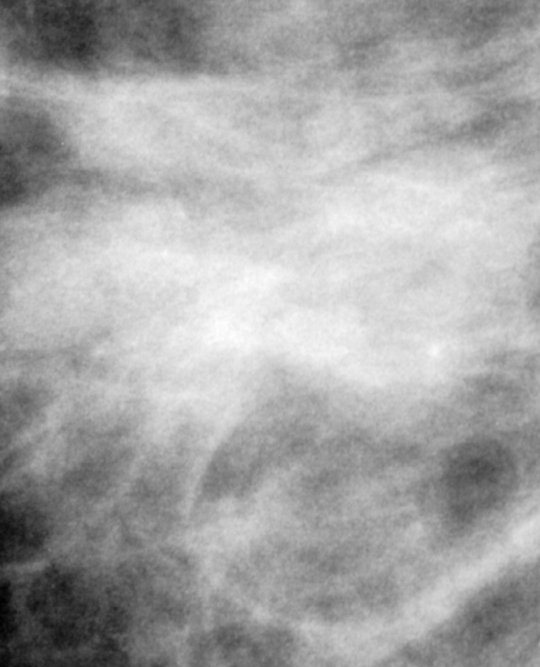
Crop from a digitized film mammogram around one marked abnormality, left breast, MLO view.
- Mass, shape irregular, margins ill defined; BI-RADS assessment category 5; subtlety rating 5 on a 1 (subtle) to 5 (obvious) scale; pathology result (as recorded, not read from the image): malignant.